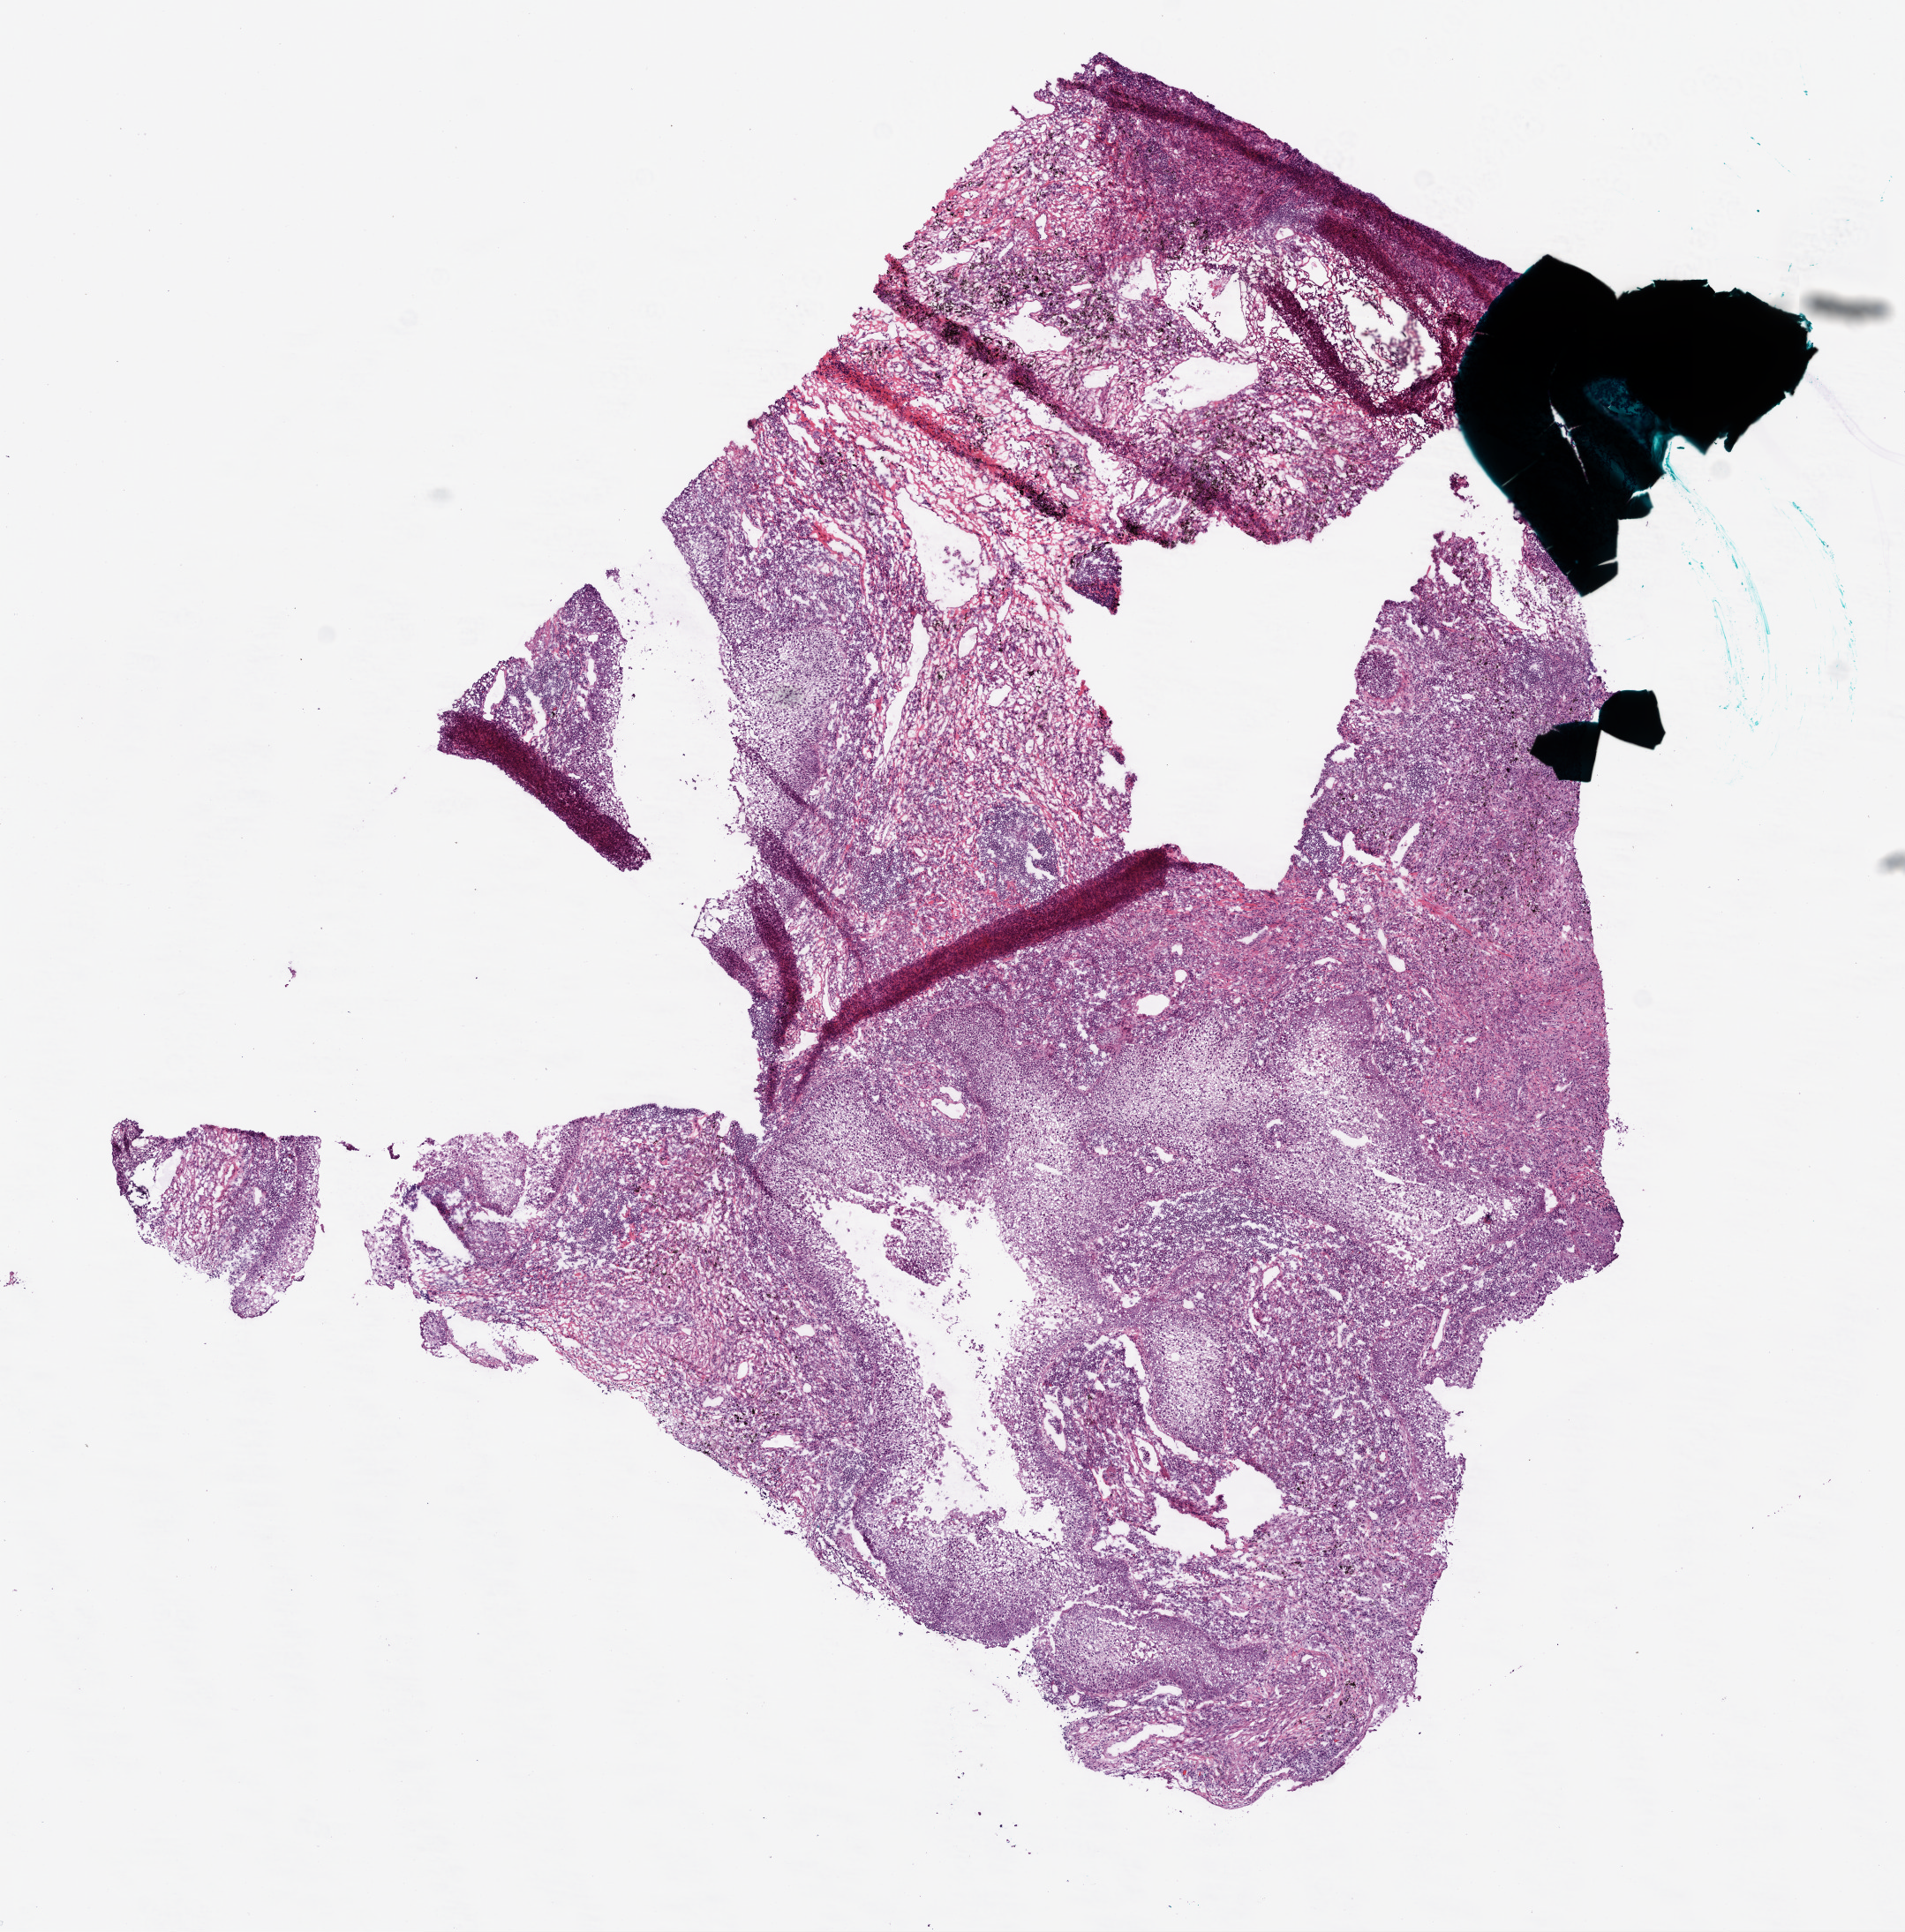
Digitized H&E tissue section (whole slide) — a low-resolution overview of the entire scanned area, about 8.7 x 8.8 mm, frozen section from the bottom of the tissue portion, primary tumour sample from the lung. Male patient; age at initial diagnosis 73 years. Composition of this section per pathologist review: tumour nuclei 60%, necrosis 5%.
- AJCC pathologic stage: IB
- TNM: T2 N0 M0
- histologic diagnosis: Squamous cell carcinoma, NOS